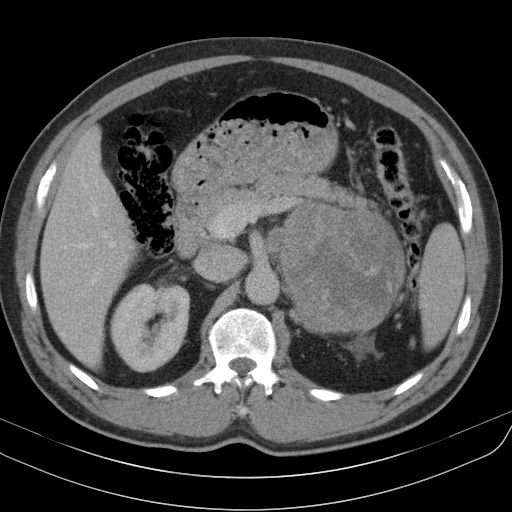
Contrast-enhanced abdominal CT, one axial slice. Position 66 of 91 along the scan axis. 130 kVp. Intravenous contrast given. Soft-tissue window (W 400 / L 40 HU). 5 mm slice thickness. 512 × 512 image matrix. Male patient, age 51 years. Case-level facts recorded for this patient, not image findings: diagnosis: adrenocortical carcinoma; tumour side: left adrenal; tumour size at pathology: 18 cm; Ki-67 index: 40 %.
Annotated regions visible in this slice (semi-automatically segmented with operator editing):
- mass: bounding box (x1, y1, x2, y2) in pixels: (276, 205, 404, 331)